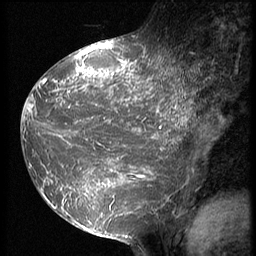
Breast MRI (dynamic contrast-enhanced), one sagittal slice. Position 27 of 64 along the scan axis. 3 images stored at this slice position (order not interpretable as contrast timing). 1.5 T. TE 4.2 ms, TR 9 ms. 2.5 mm slice thickness. 256 × 256 image matrix, field of view 180 × 180 mm. Patient: female, 39 years. From the clinical record (not read from this slice): setting: breast cancer imaged before/during neoadjuvant chemotherapy; receptor status: HER2-positive.
Annotated regions visible in this slice (semi-automatically segmented with operator editing):
- analysis volume of interest (the breast-tissue region the enhancement analysis was run in; not a lesion): box from (x=23, y=47) to (x=191, y=239) px
- tumour enhancement mask (voxels above the 140 % enhancement threshold inside the analysis volume of interest): (x=23, y=47)–(x=191, y=229)